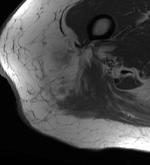
MRI of an extremity soft-tissue mass, one axial slice. Slice 12 of 56 in the series (ordered by position). MR volume resampled by the dataset authors to the PET/CT grid (not the native acquisition matrix). 3.27 mm slice thickness. 150 × 165 image matrix. Female patient. From the clinical record (not read from this slice): histological type: epithelioid sarcoma with vascular differentiation; site of the primary tumour: right buttock.
Annotated regions visible in this slice (expert contour drawn on MRI and transferred to this co-registered scan by the dataset authors):
- gross tumour volume (mass): box from (x=48, y=54) to (x=76, y=112) px